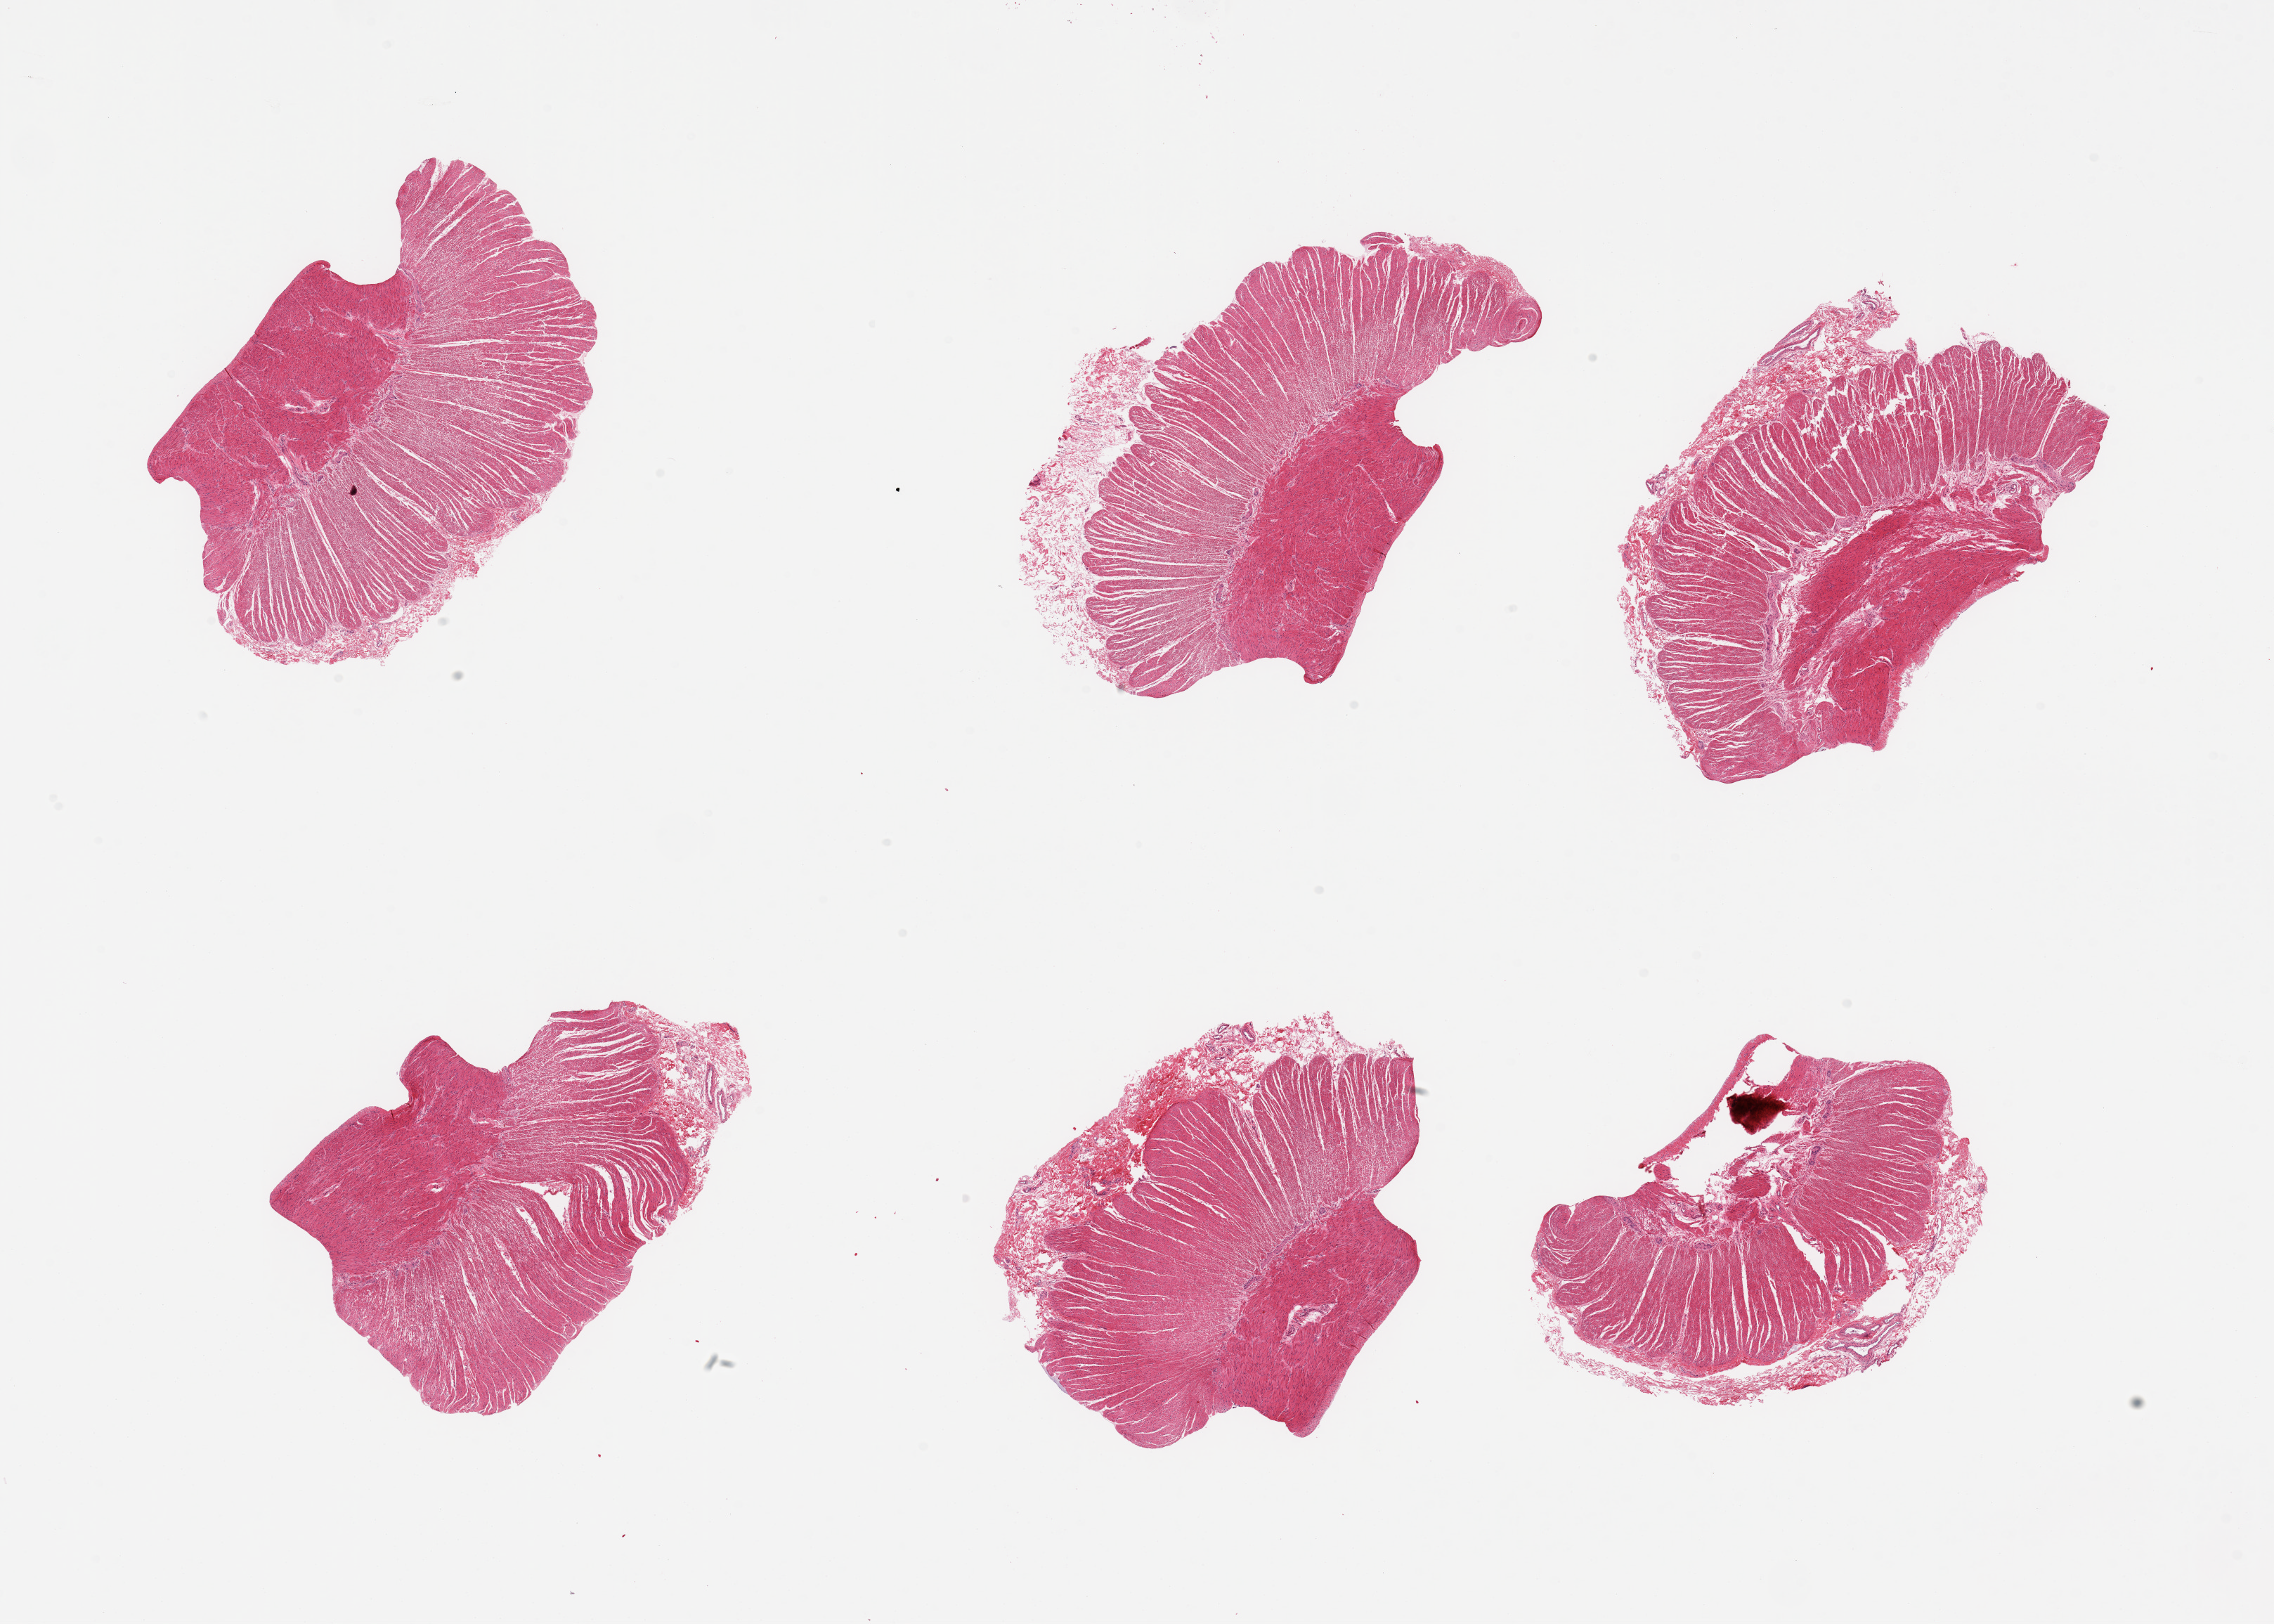
Digitized haematoxylin and eosin-stained section, brightfield, shown as a low-resolution overview of the whole scanned area (about 25.6 x 18.3 mm); PAXgene-fixed, paraffin-embedded tissue; section of sigmoid colon (target tissue); donor tissue sample.
Pathologist's review note for this sample: 6 pieces; target muscularis.